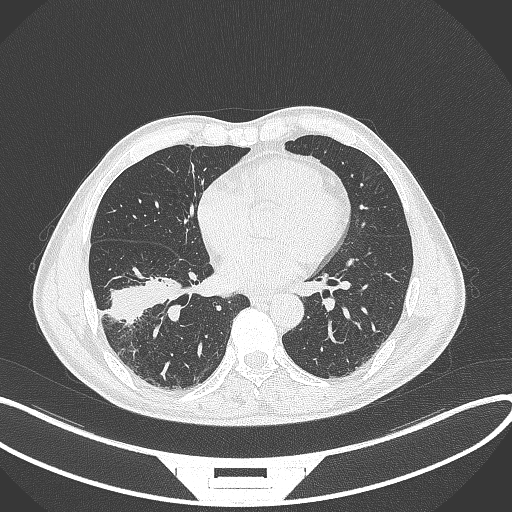
Chest CT, one axial slice. Position 151 of 364 along the scan axis. Reconstruction kernel B70f. 120 kVp. Lung window (W 1500 / L -600 HU). 1 mm slice thickness. 512 × 512 image matrix, field of view 400 × 400 mm. Patient: male, 58 years. Case-level facts recorded for this patient, not image findings: clinical TNM (as recorded): T3 N0 M0; histopathological grade: G2.
Structures marked on this image (rectangle marked by the reading radiologist):
- lung tumour (recorded histology: squamous cell carcinoma): bounding box (x1, y1, x2, y2) in pixels: (105, 274, 186, 322)